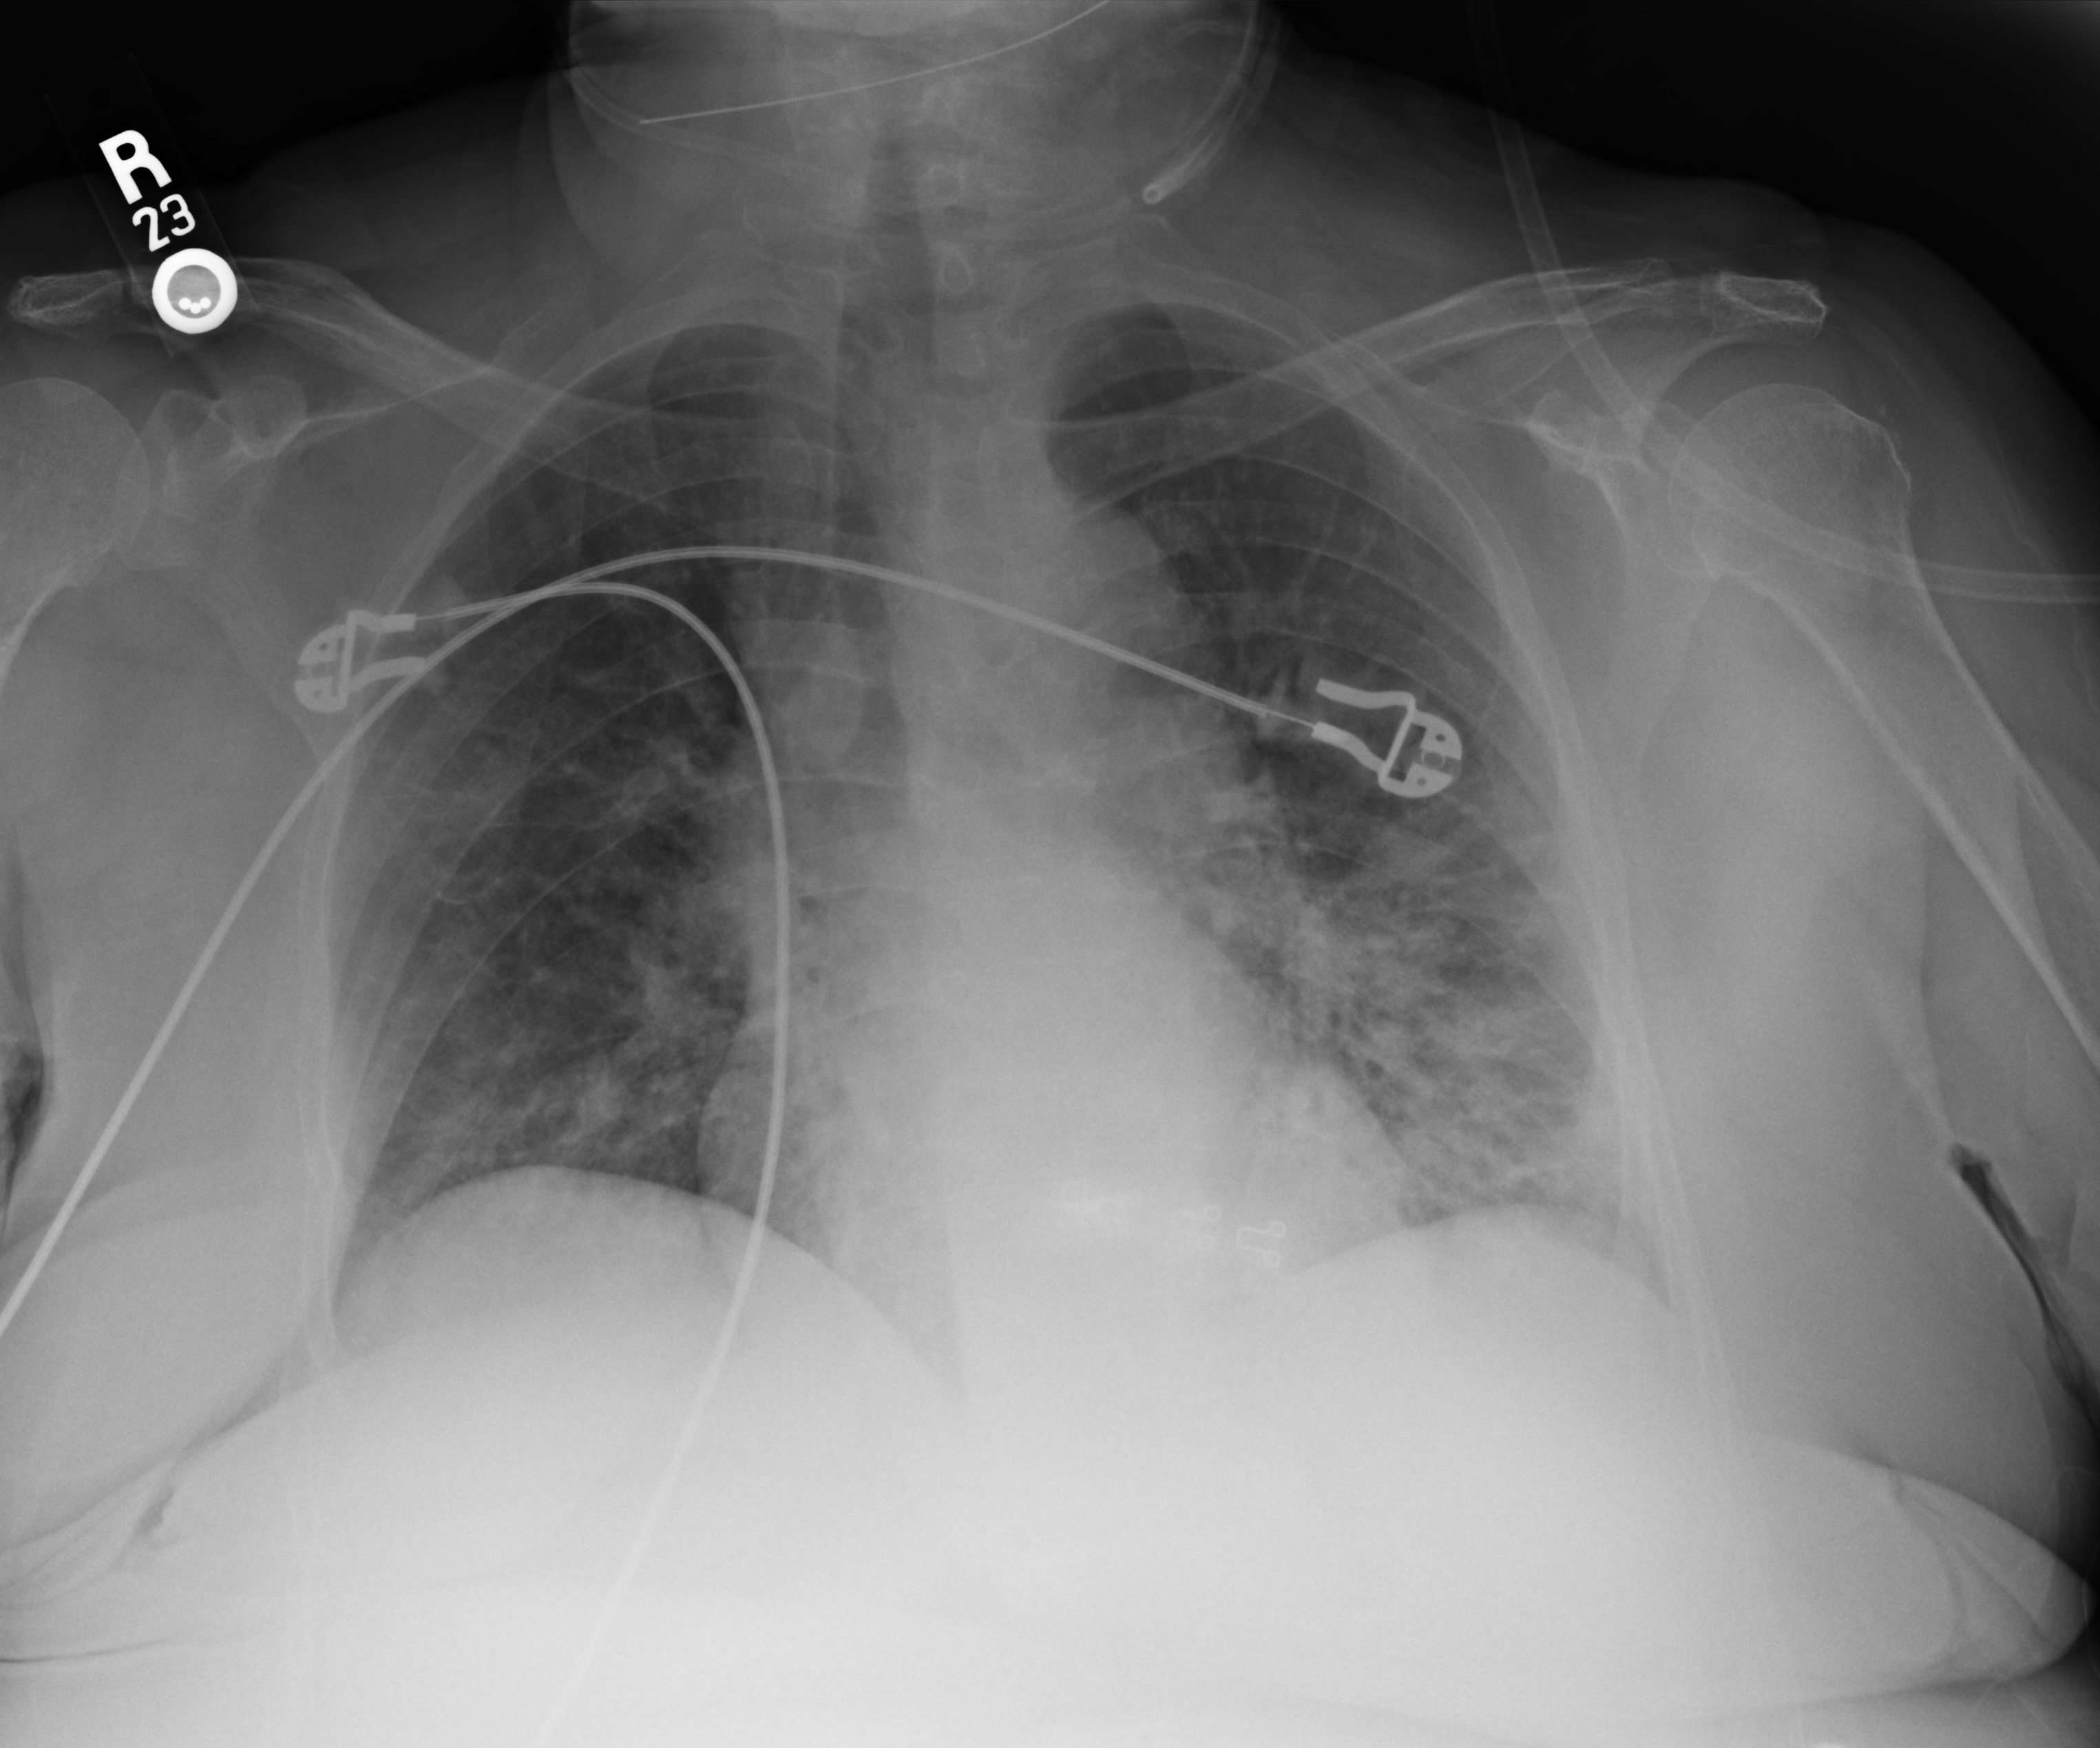
Chest X-ray (portable). Patient hospitalised with COVID-19; female, aged 60–74 years.
Hospital-stay facts (about this admission, not read from this image; timing relative to this image not recorded):
- mechanically ventilated during this hospital stay: yes
- admitted to intensive care during this hospital stay: yes
- hypertension (admission record): yes